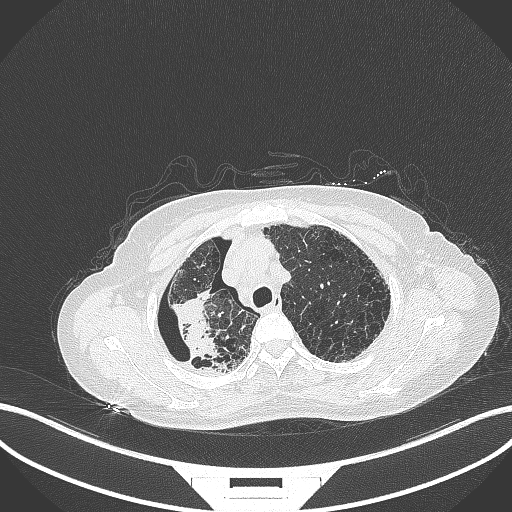
Chest CT, one axial slice. Slice 287 of 408 in the series (ordered by position). Reconstruction kernel B70f. Lung window (W 1500 / L -600 HU). 1 mm slice thickness. 512 × 512 image matrix, field of view 400 × 400 mm. Female patient, age 64 years. From the clinical record (not read from this slice): clinical TNM (as recorded): T3 N3 M0.
Outlined on this slice (bounding box drawn by a radiologist):
- lung tumour (recorded histology: squamous cell carcinoma): bounding box (x1, y1, x2, y2) in pixels: (168, 286, 223, 371)